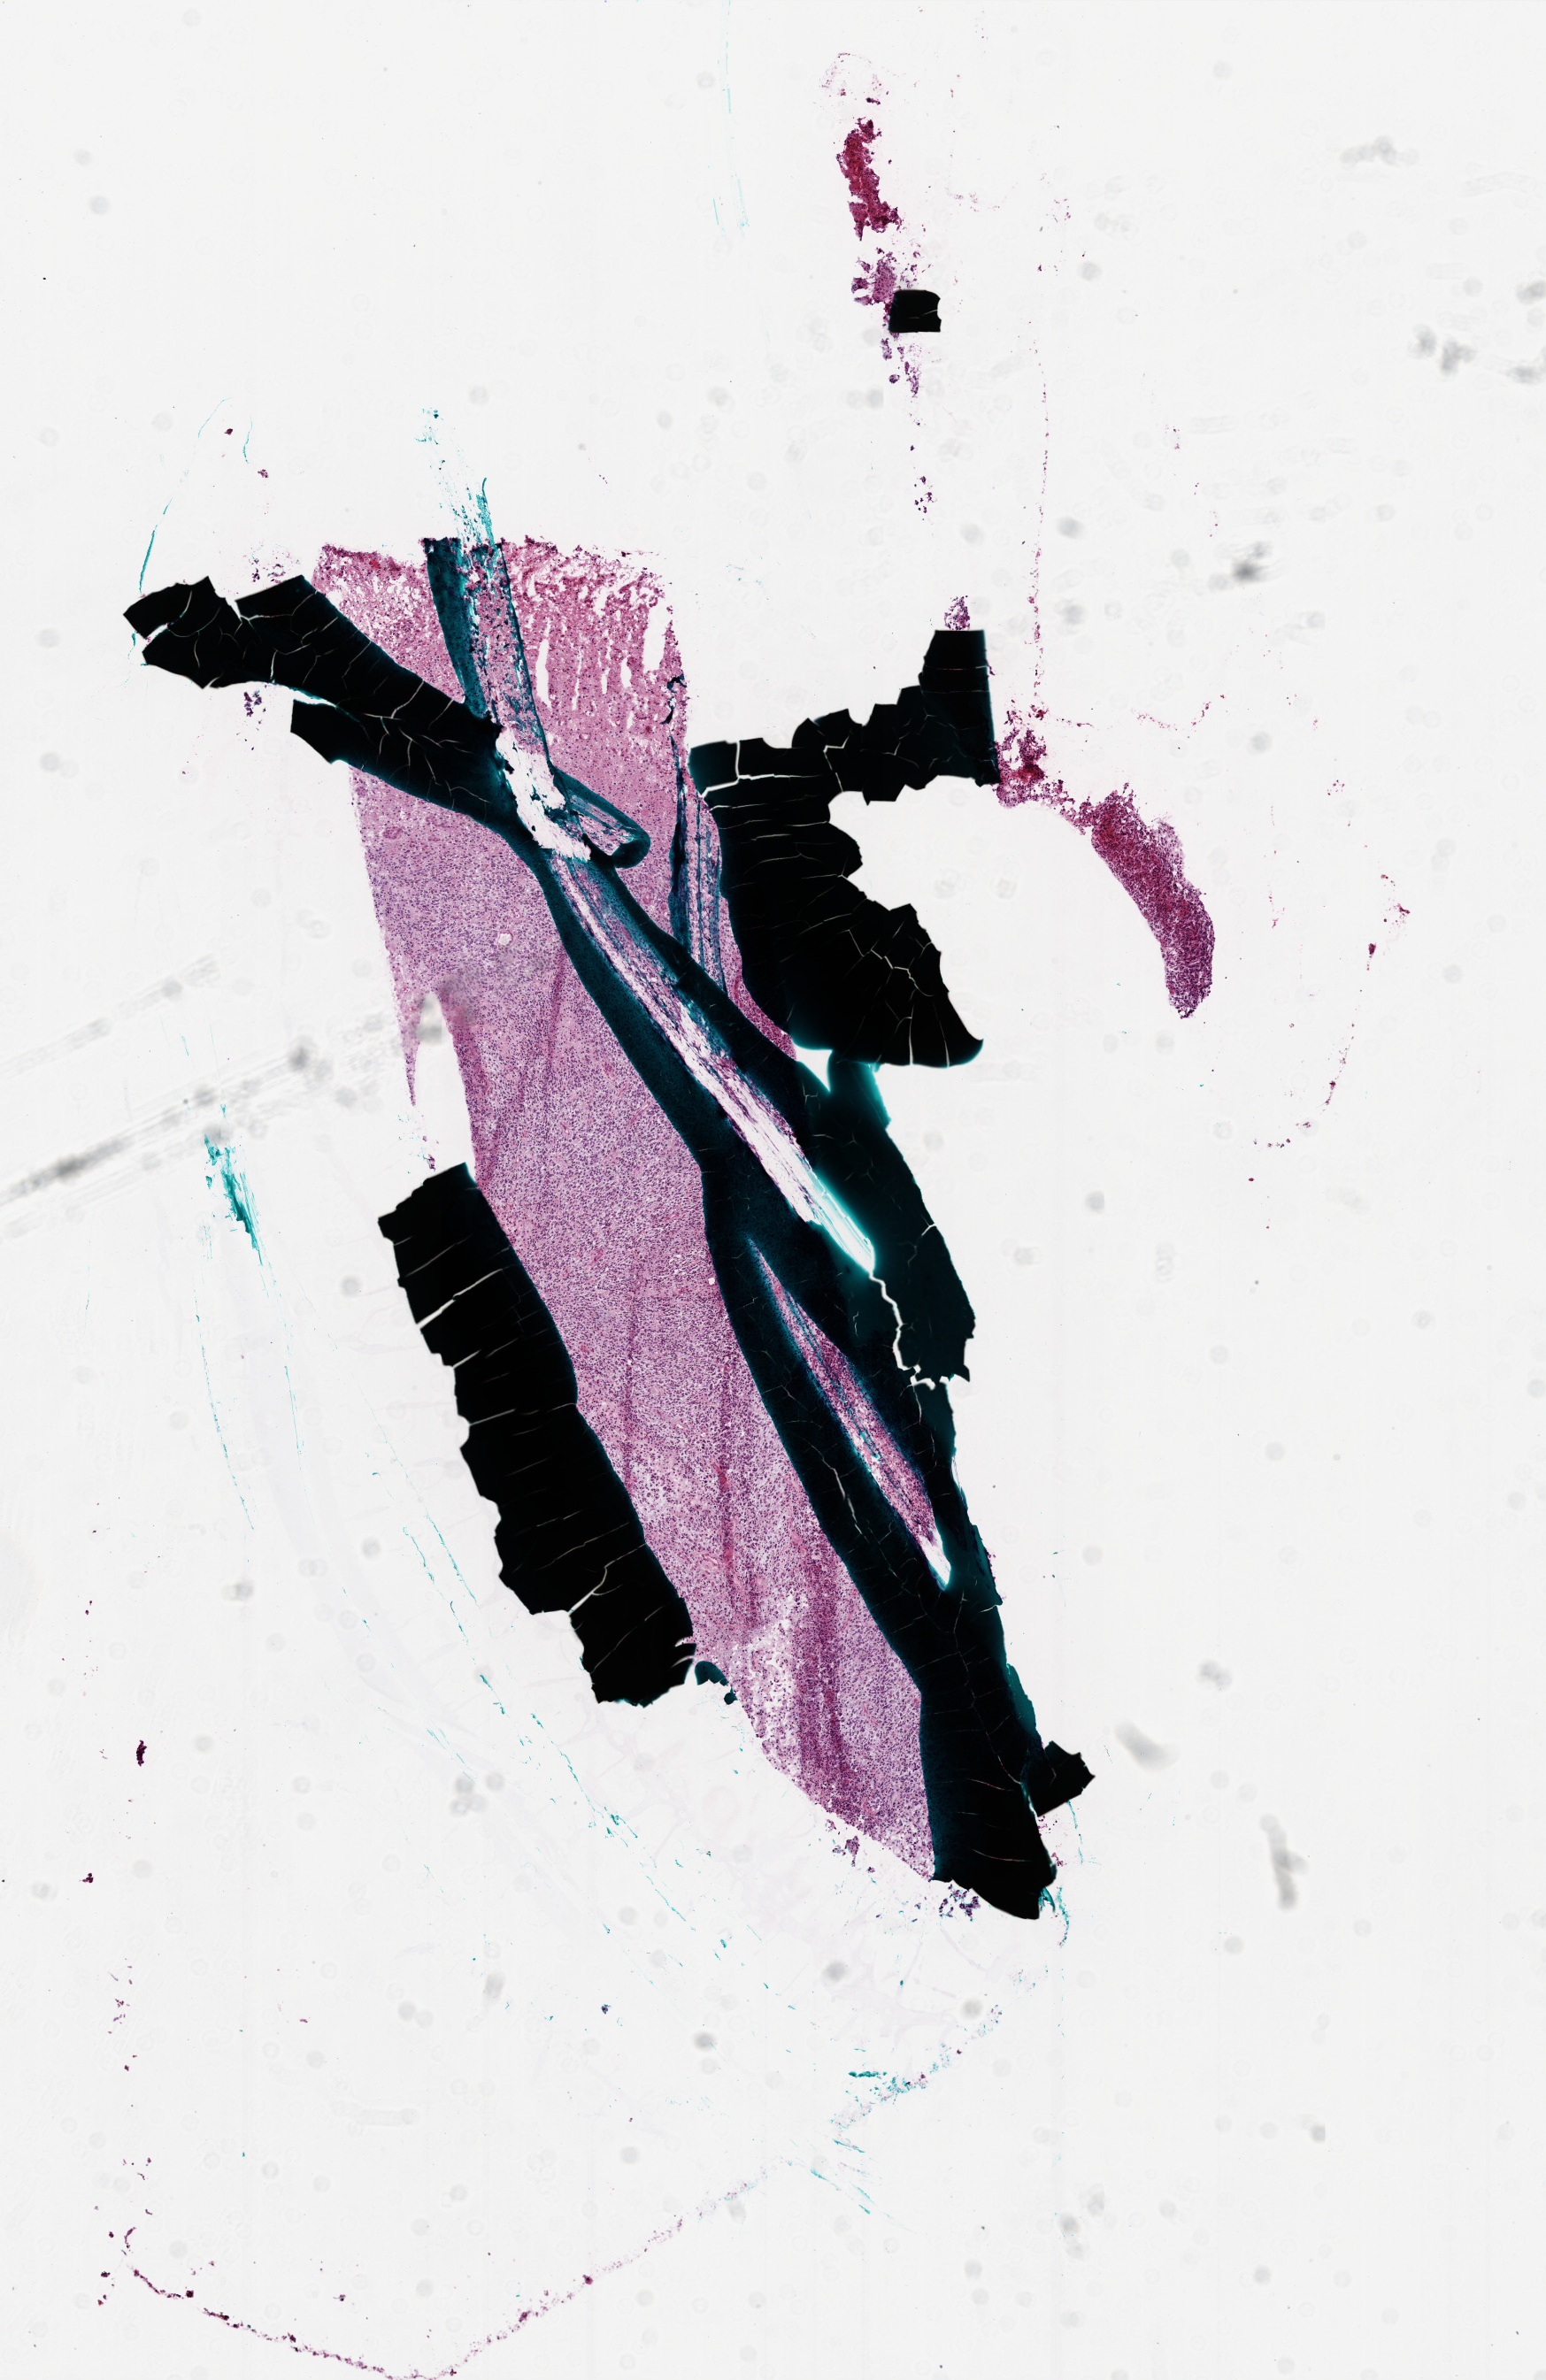
Digitized H&E-stained tissue section (whole slide) — shown as a low-resolution overview of the whole scanned area (about 7.0 x 10.8 mm, from a 20x scan), frozen section, brain, primary tumour sample. Male, age 54 years at initial diagnosis. Pathologist review of this section (percent, as recorded): tumour cells 80%, tumour nuclei 95%, normal cells 0%, stromal cells 10%, necrosis 10%.
Diagnosis: Glioblastoma.